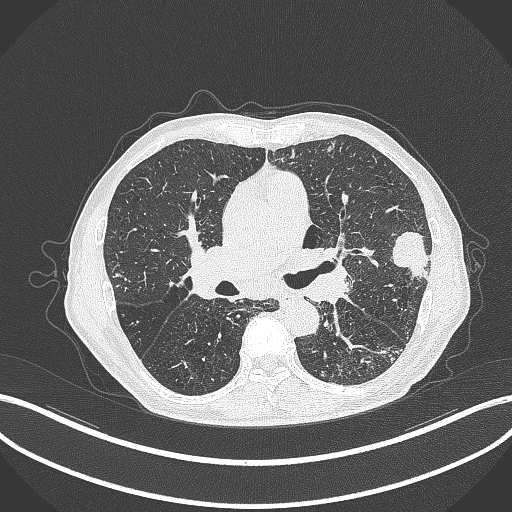
Chest CT, one axial slice; position 235 of 463 along the scan axis; reconstruction kernel B70f; 120 kVp; lung window (W 1500 / L -600 HU); 1 mm slice thickness; 512 × 512 image matrix. Male patient, age 74 years. From the clinical record (not read from this slice): clinical TNM (as recorded): T2a N1 M0.
Annotated regions visible in this slice (rectangle marked by the reading radiologist):
- lung tumour (recorded histology: adenocarcinoma): box from (x=387, y=226) to (x=430, y=283) px